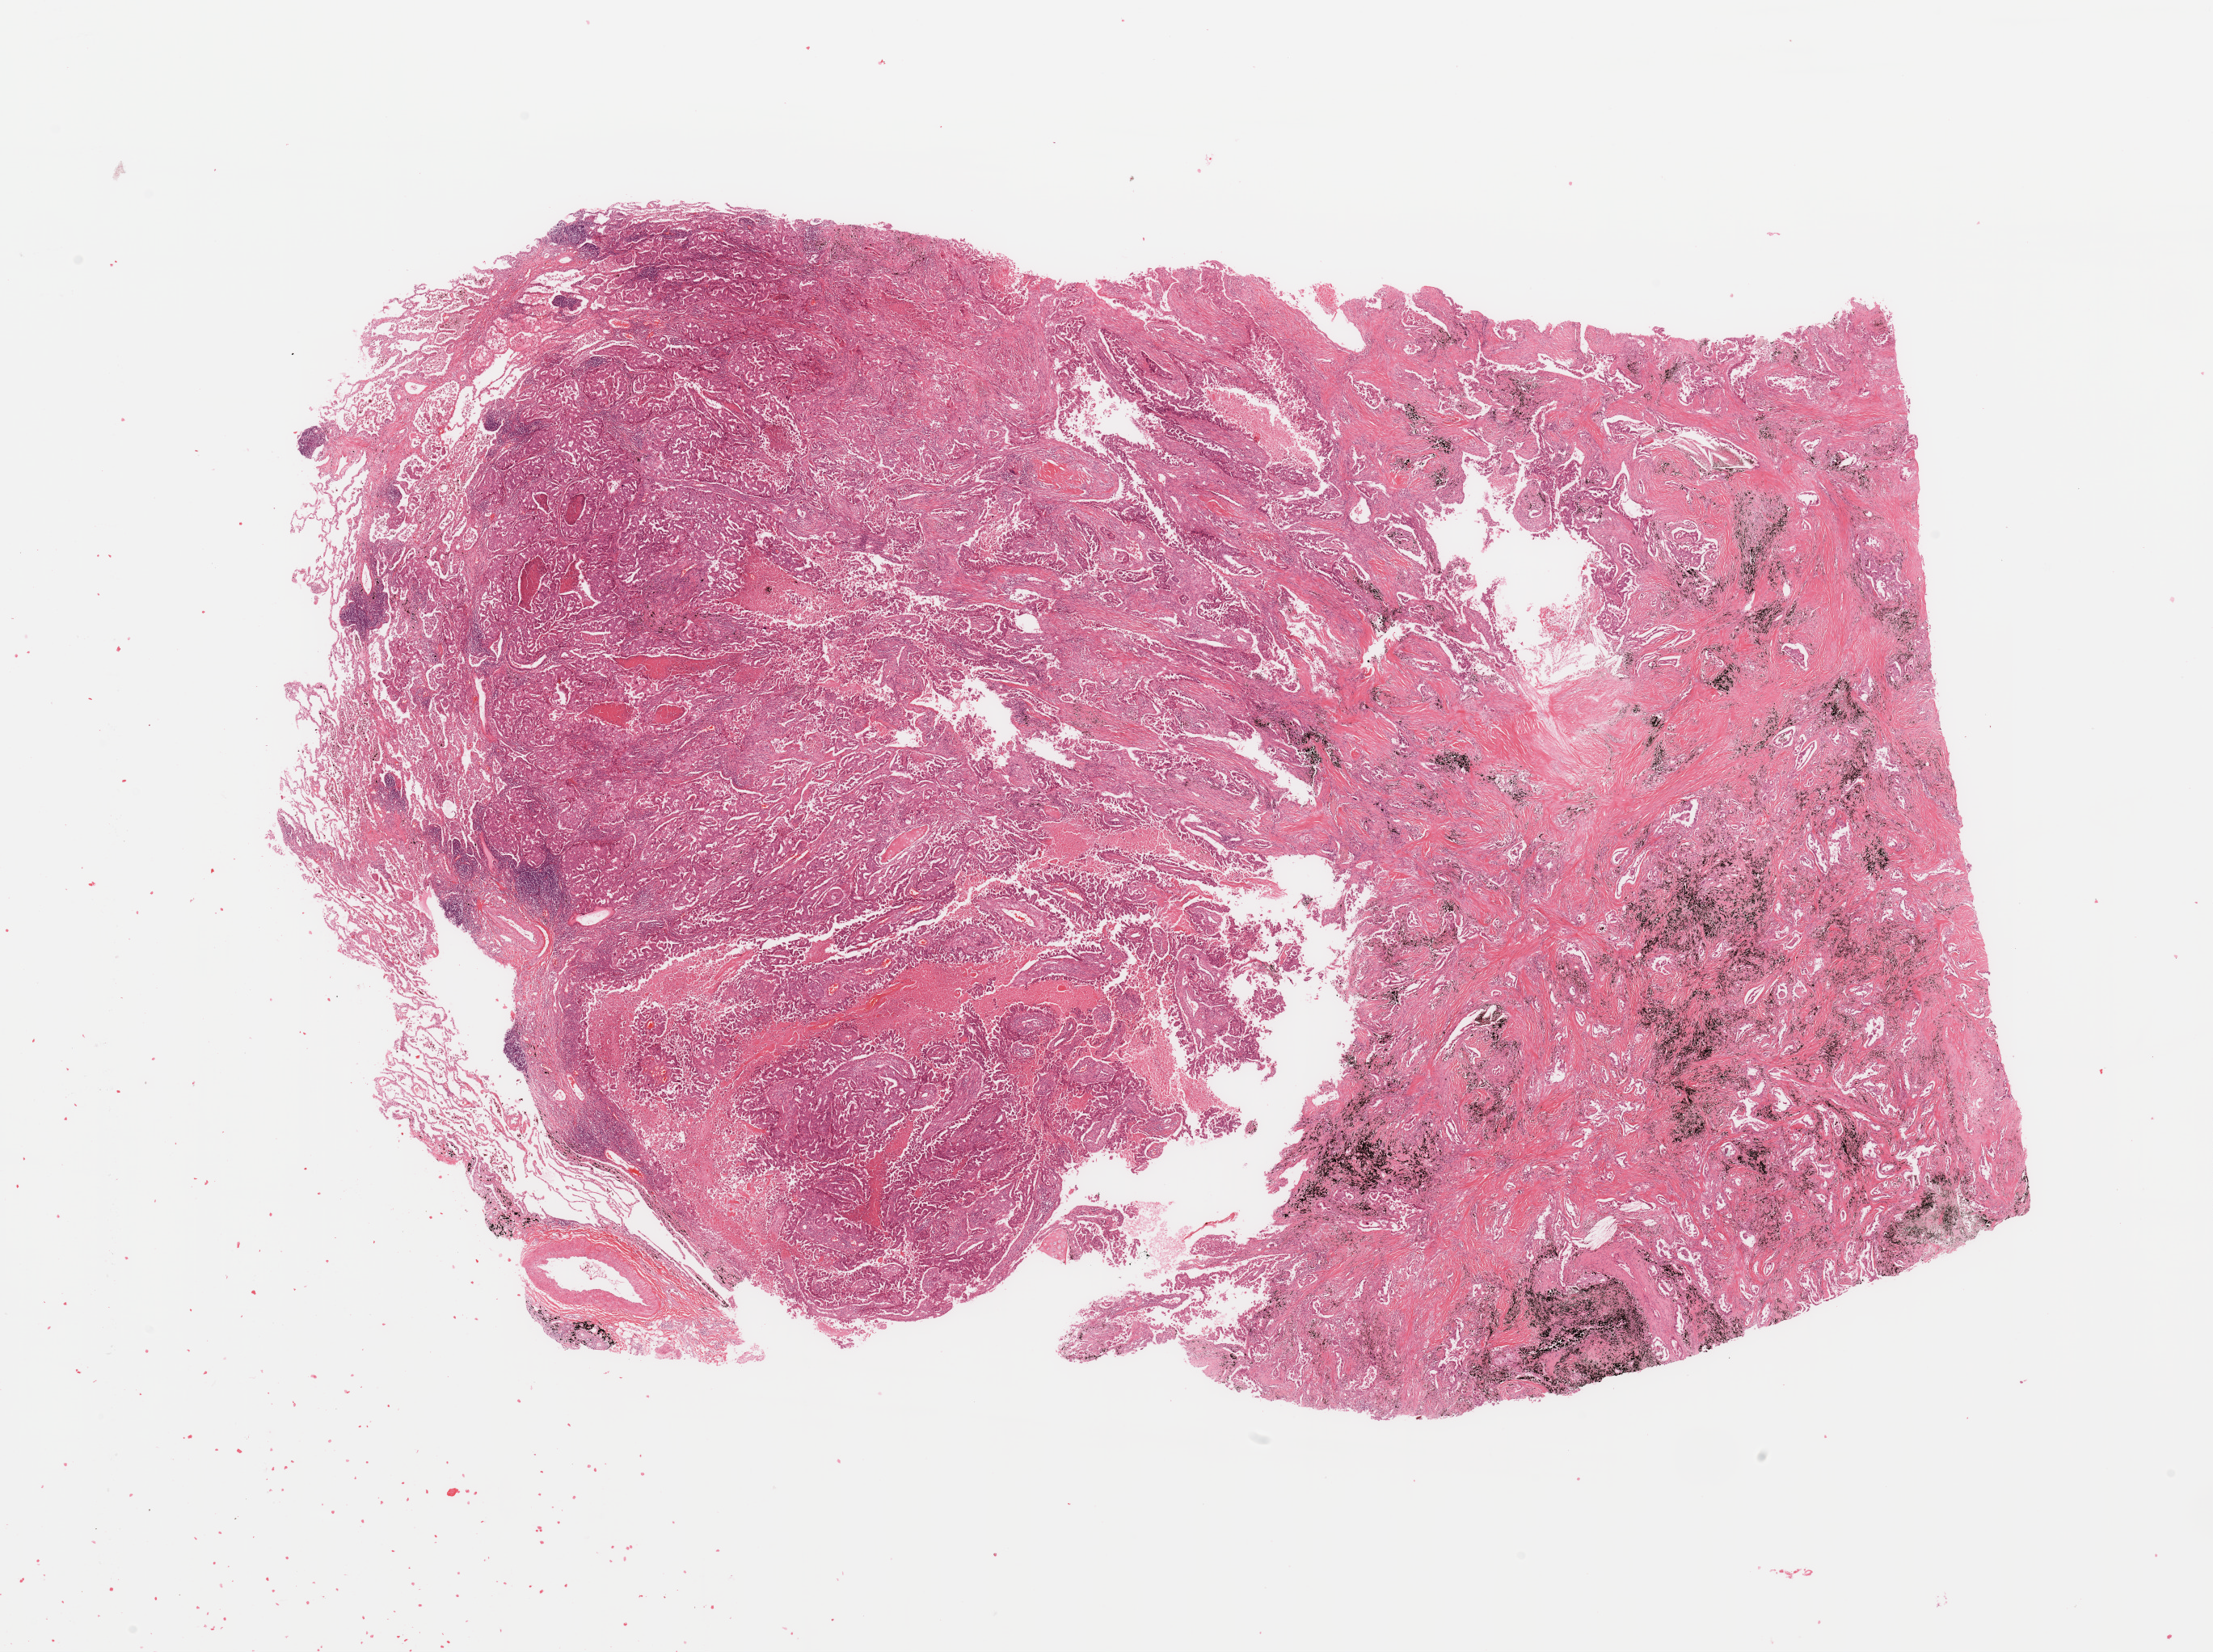
Digitized H&E-stained tissue section (whole slide), a low-resolution overview of the entire scanned area, about 21.7 x 16.2 mm (from a 20x scan). Tumour tissue sample, sampled site: lung. Patient: male, age 56 years. Histologic grade: G3 (poorly differentiated). Composition of this section per pathologist review: tumour nuclei 65%, necrosis 5%.
AJCC pathologic stage: IB. Primary tumour site (as recorded): right upper lobe. Diagnosis: Adenocarcinoma, NOS.